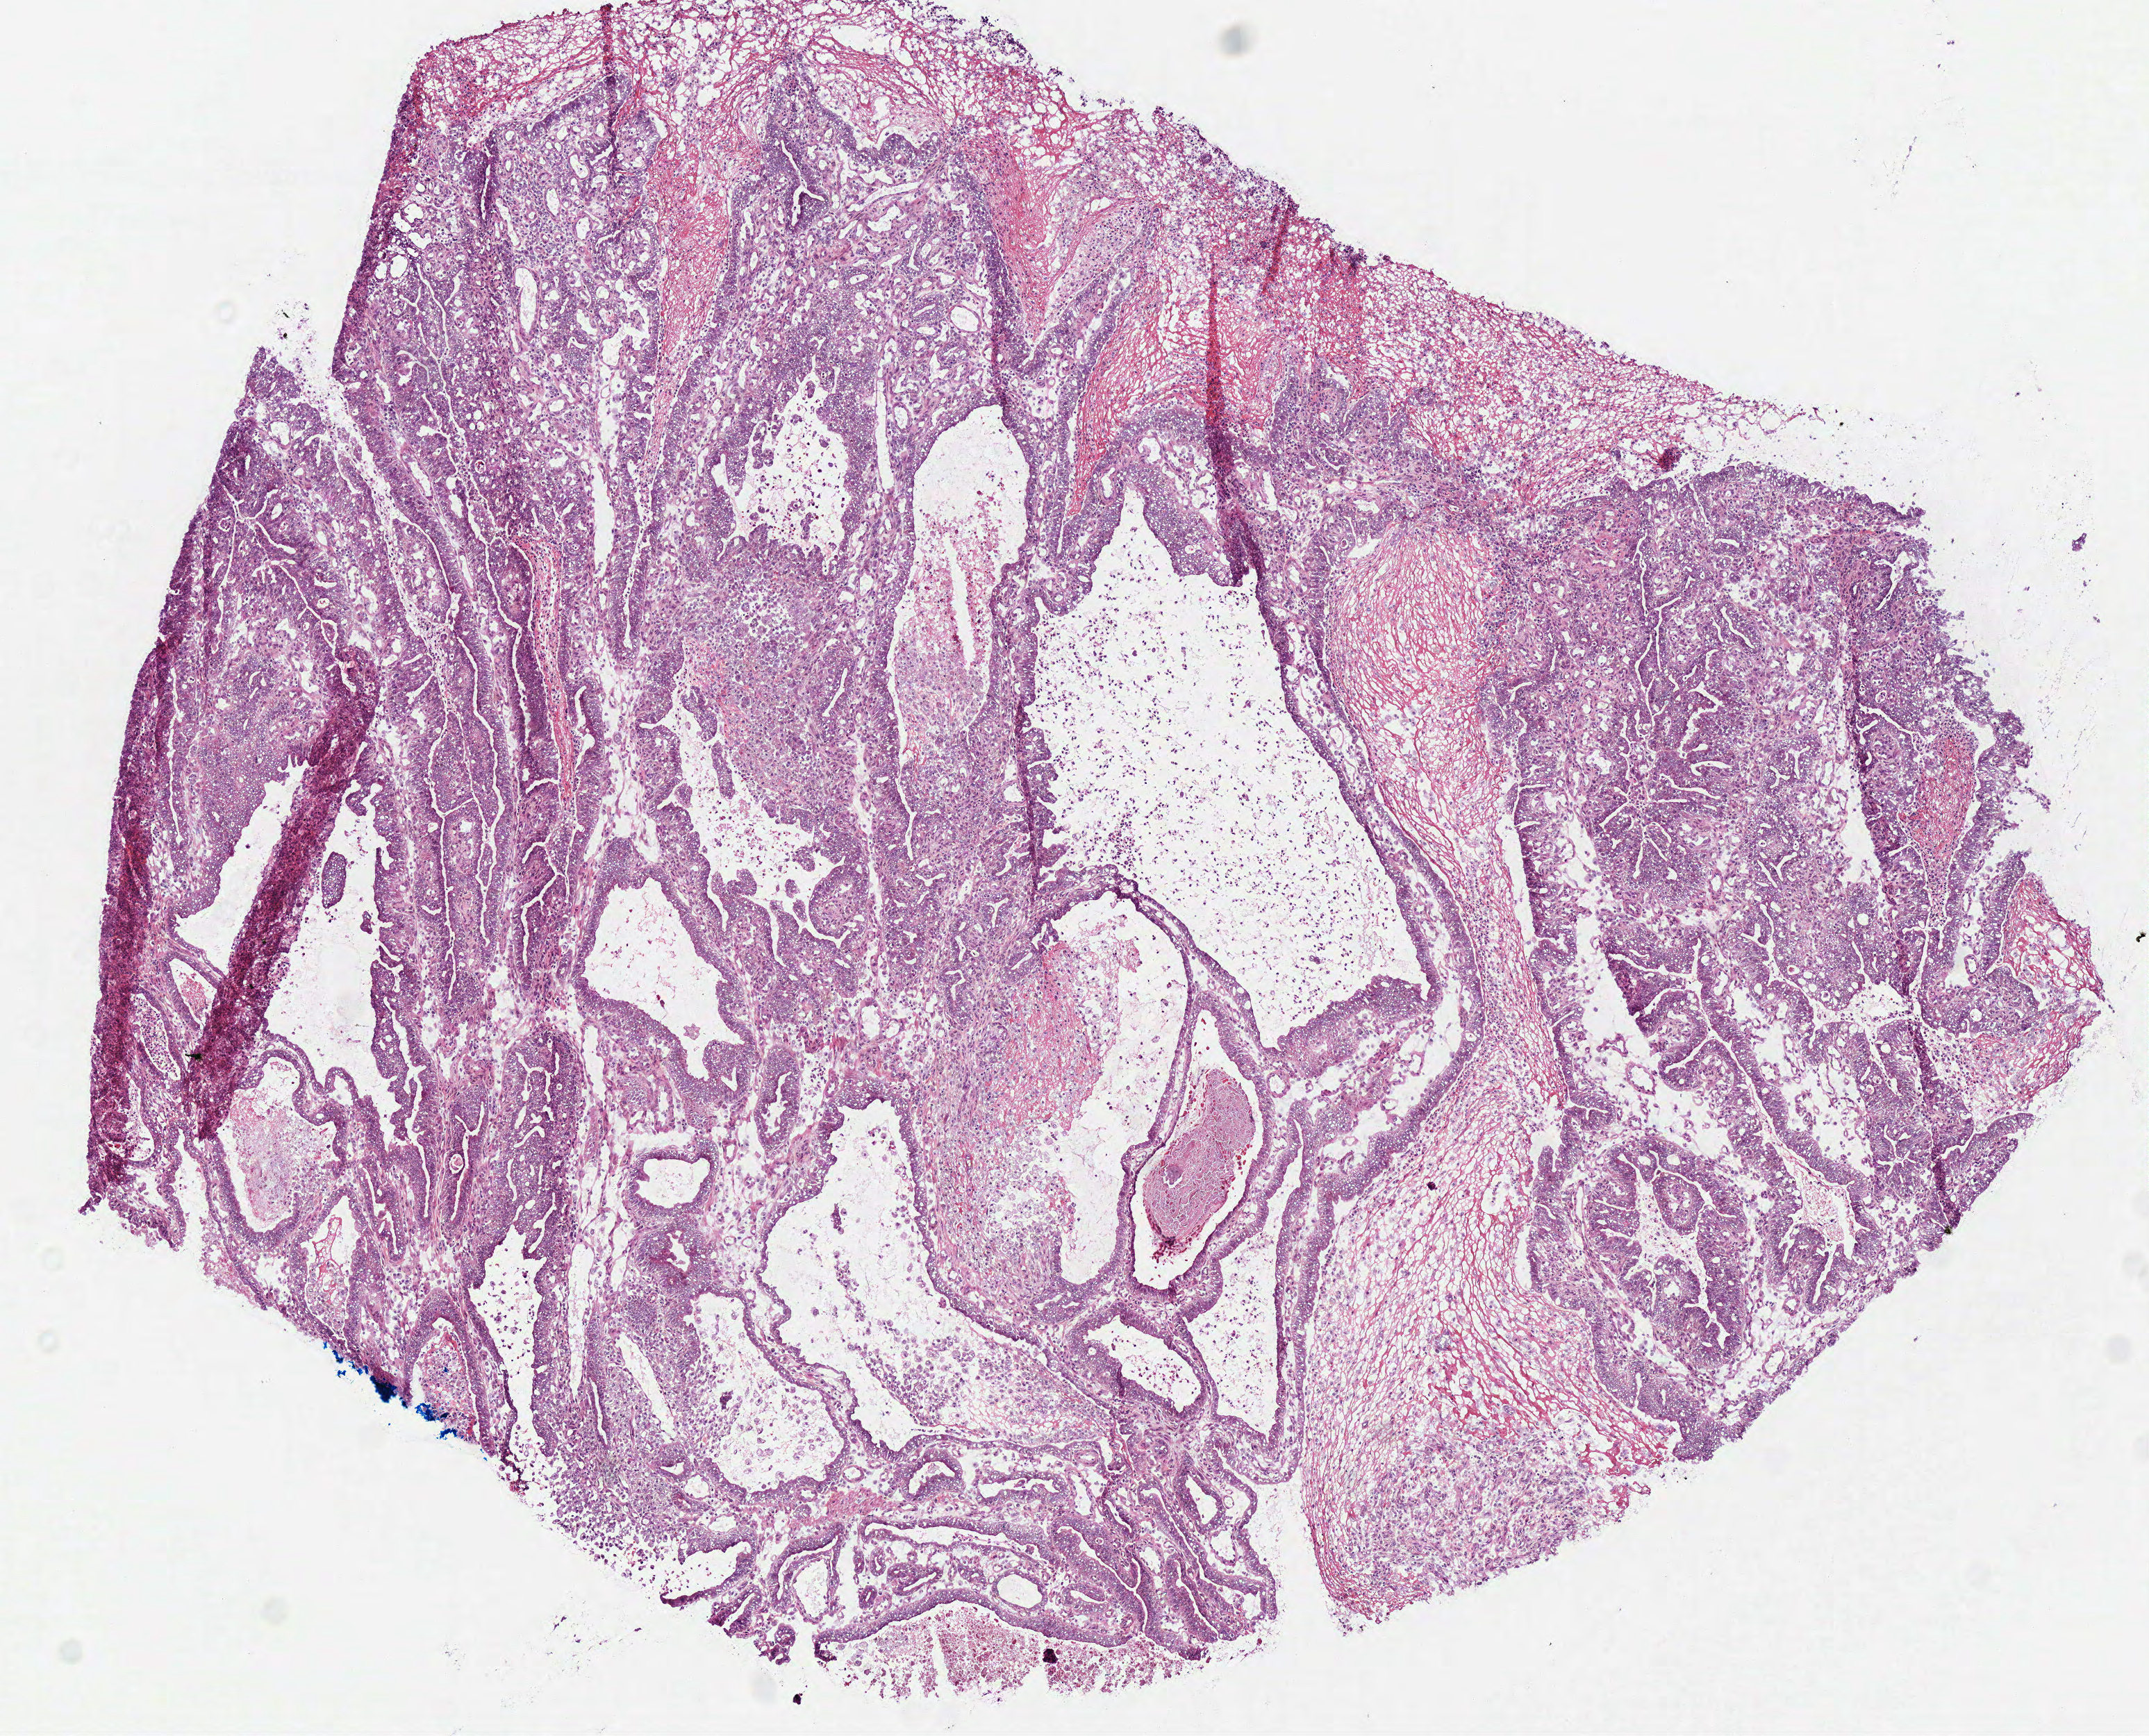
Digitized Hematoxylin and eosin (H&E) stained tissue section (whole slide) — a low-resolution overview of the entire scanned area, about 6.1 x 4.9 mm; frozen section from the bottom of the tissue portion; primary tumour sample from the stomach. Patient: male, age at initial diagnosis 64 years. Histologic grade: G2 (moderately differentiated). Slide review estimates, as recorded: tumour cells 80%, tumour nuclei 65%, normal cells 0%, stromal cells 15%, necrosis 5%.
AJCC pathologic stage: IIB (6th edition). Pathologic diagnosis: Tubular adenocarcinoma (body of stomach). Lymph nodes positive (case pathology): 5 of 14 examined.